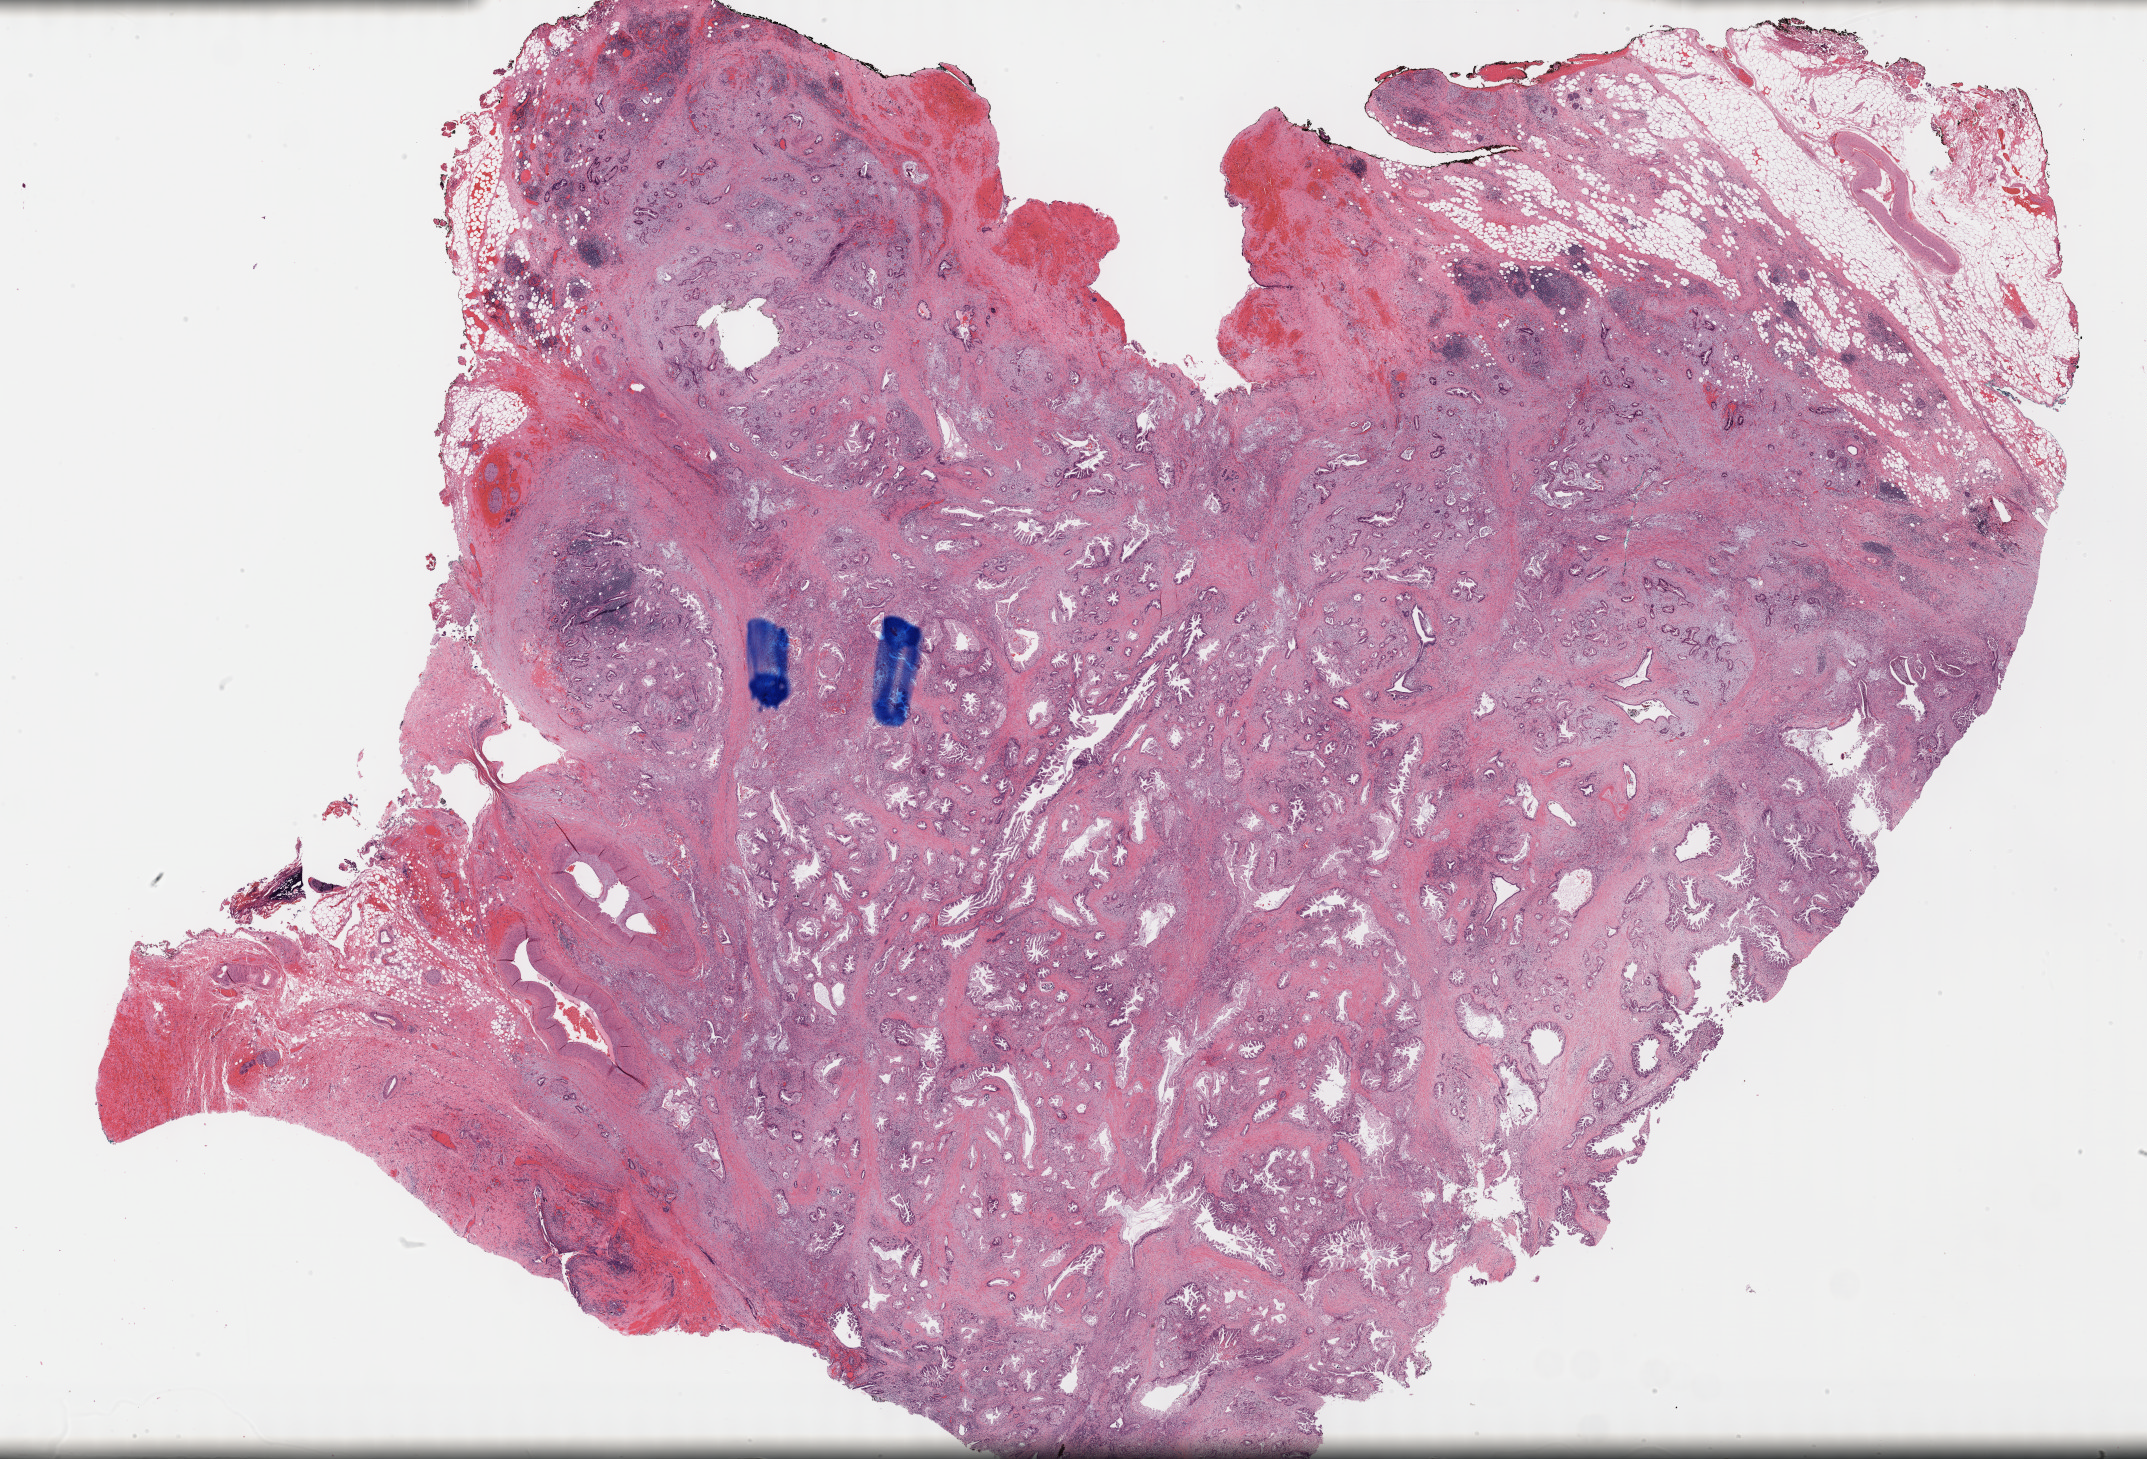
Hematoxylin and eosin (H&E) stained whole-slide image — shown as a low-resolution overview of the whole scanned area (about 34.7 x 23.6 mm), formalin-fixed paraffin-embedded (FFPE) diagnostic section, sample: primary tumour, pancreas. Male patient; age at initial diagnosis 67 years.
Pathologic diagnosis: Infiltrating duct carcinoma, NOS (head of pancreas).